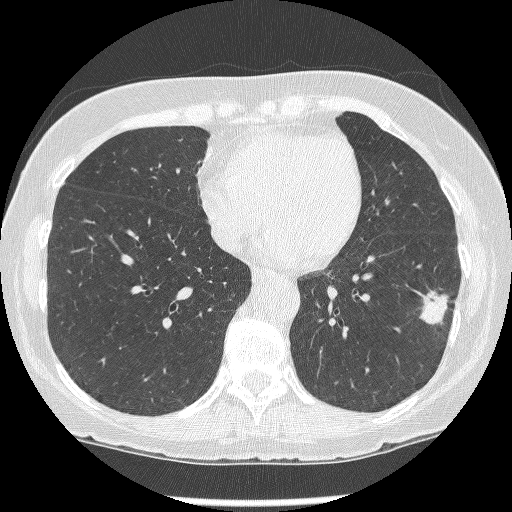
Low-dose screening chest CT, axial slice; baseline annual screen; lung window (W 1500 / L -600 HU); 1.25 mm slice thickness; lung (sharp) reconstruction kernel (BONE); 120 kVp; 512 × 512 image matrix. Female participant, aged 62 years at enrolment.
Lesion marked by an expert reader, bounding box (x1, y1, x2, y2) in pixels: (419, 282, 461, 331). The screening reader recorded 2 non-calcified nodules or masses ≥4 mm on this exam (left lower lobe, left lower lobe); which of them this box marks is not recorded. Participant outcome: lung cancer diagnosed 15 days after this screen — non-small cell carcinoma, left lower lobe, stage IIIB (AJCC 6th edition), 23 mm at pathology.